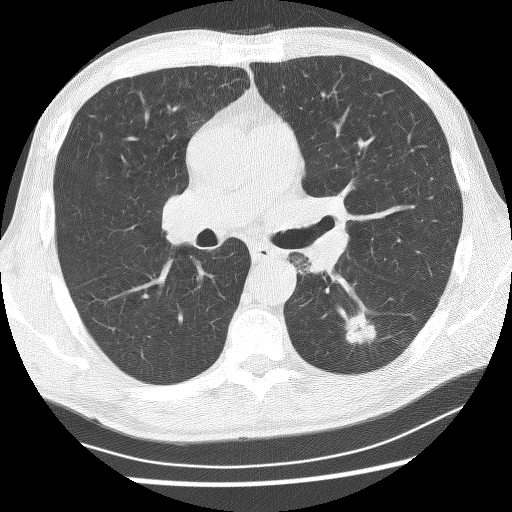
Low-dose screening chest CT, one axial slice; slice 144 of 253 in the series (ordered by position); reconstruction kernel BONE; 120 kVp; lung window (W 1500 / L -600 HU); 512 × 512 image matrix, field of view 340 × 340 mm.
Outlined on this slice (expert manual segmentation):
- lesion 1 (tumor, lower lobe of left lung): bounding box (x1, y1, x2, y2) in pixels: (346, 312, 376, 344)